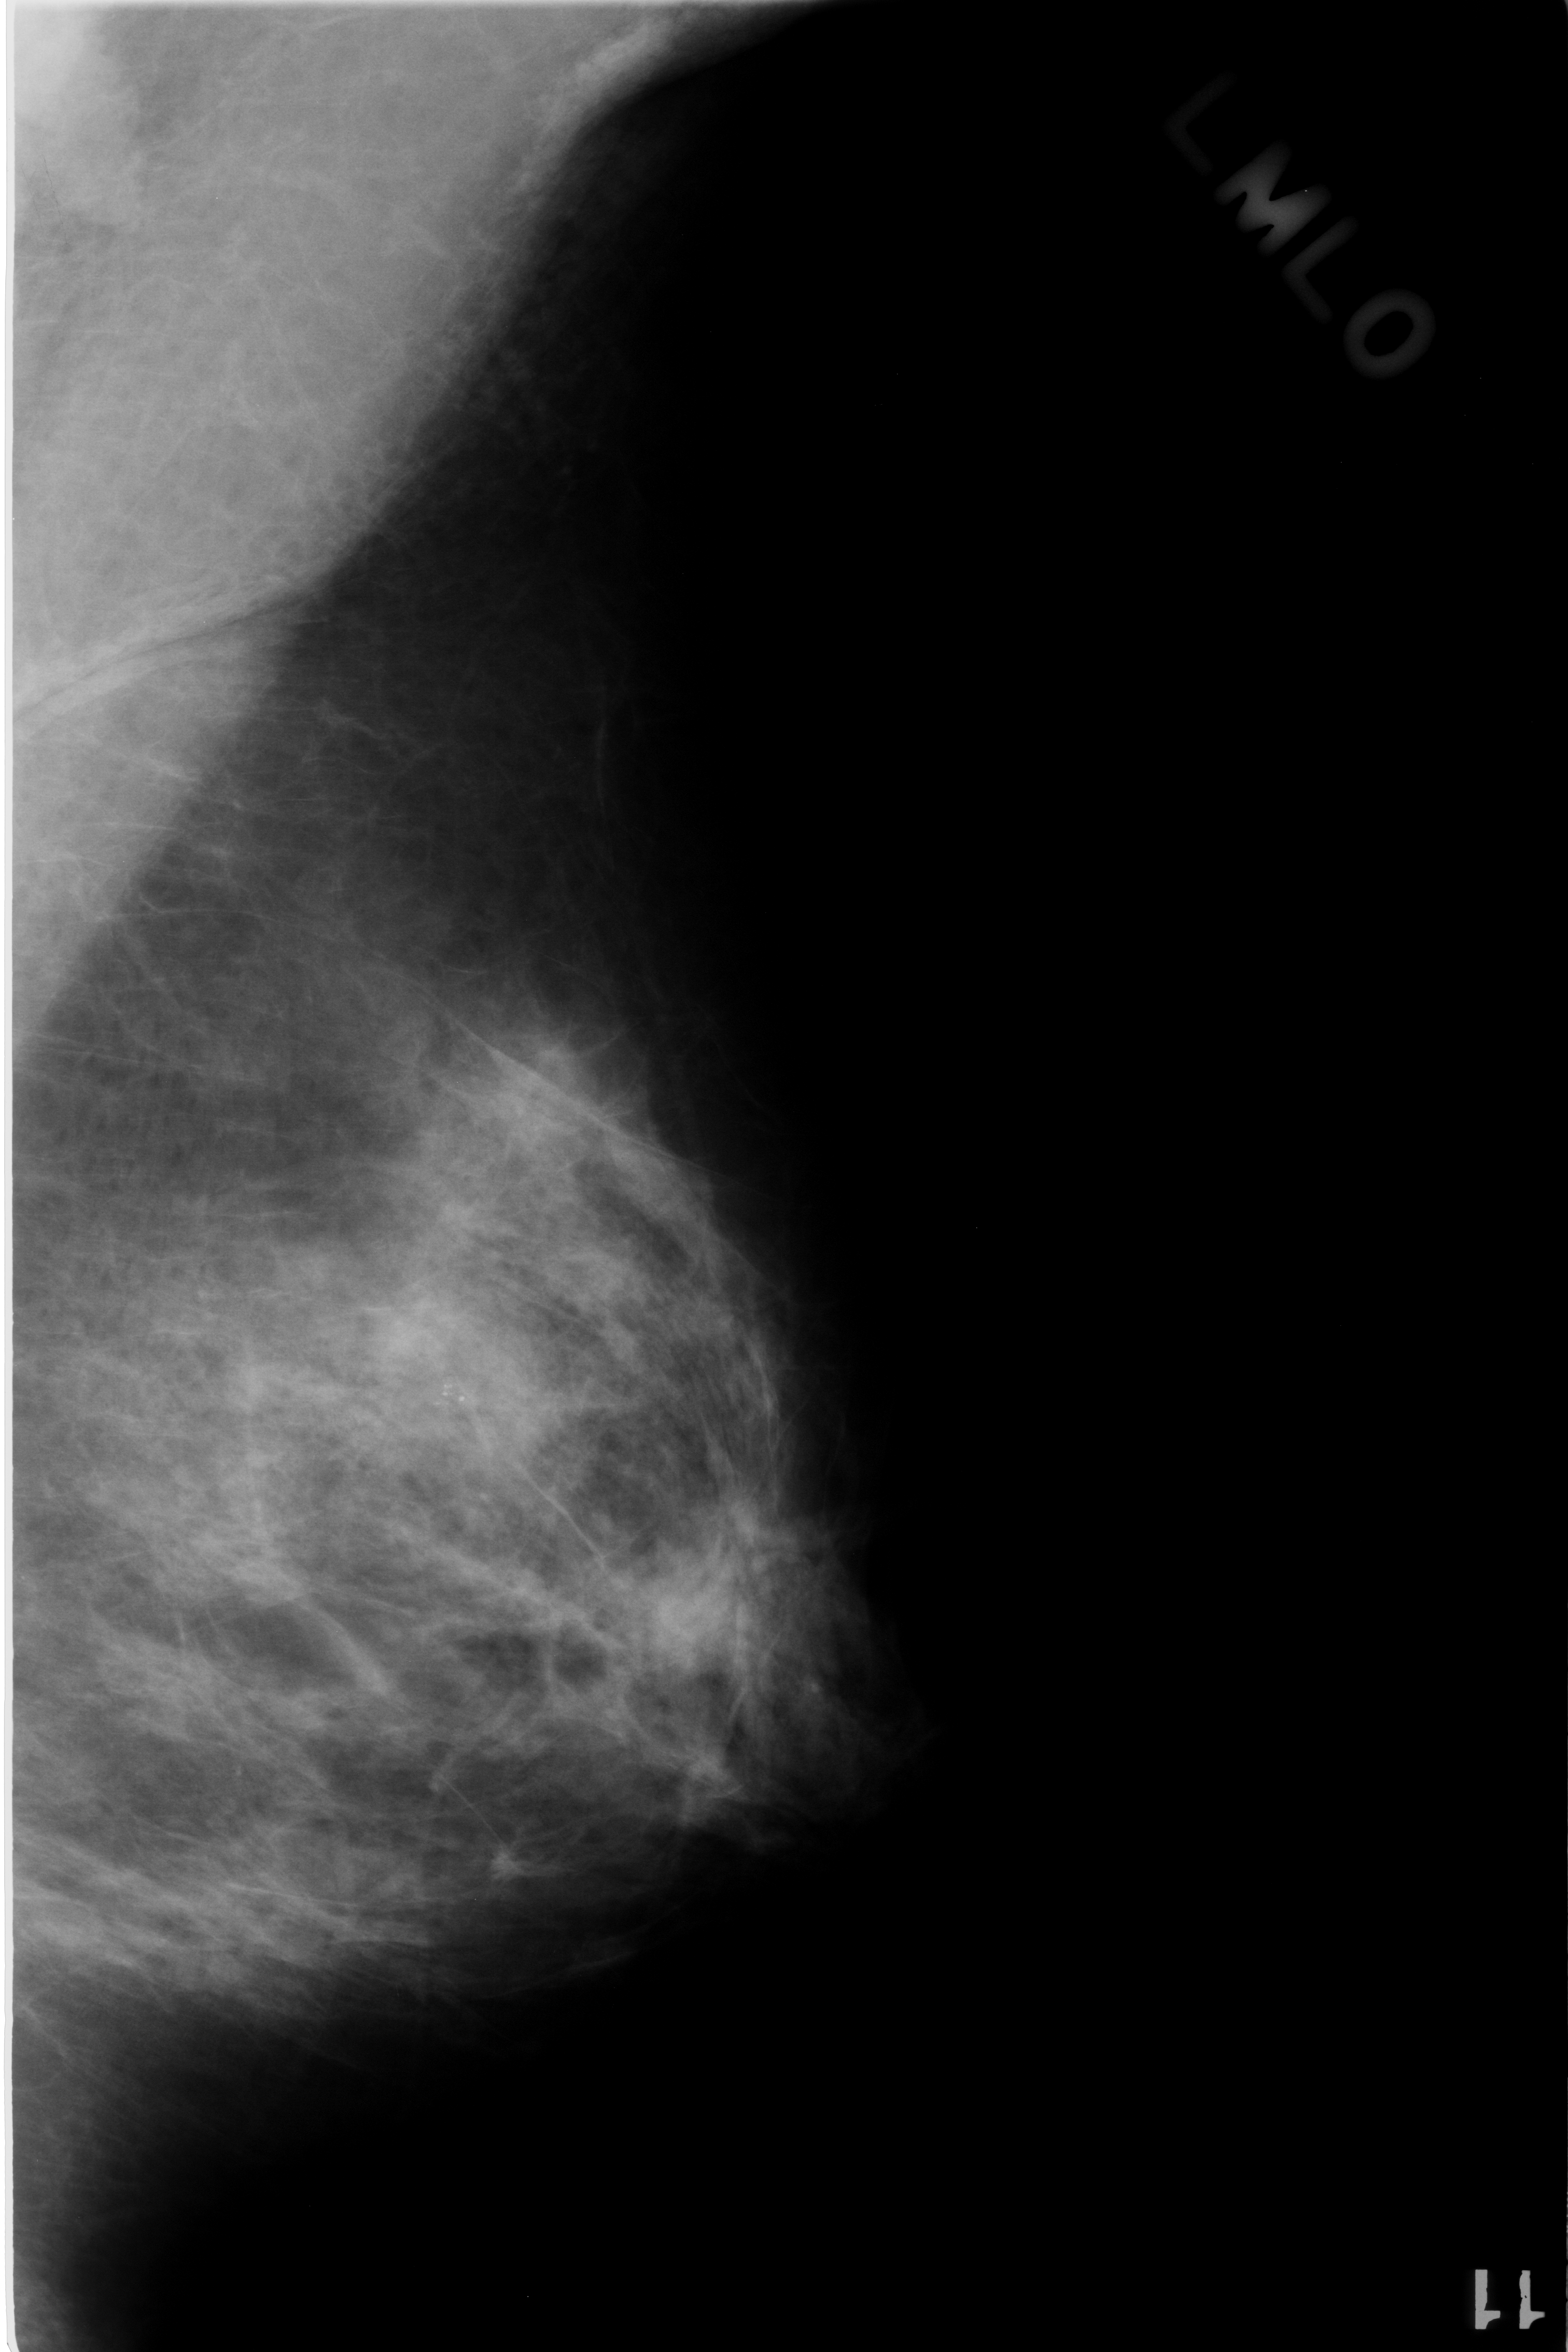
Mammogram (digitized film); left breast; mediolateral oblique (MLO) view; BI-RADS breast density category 2 (scale 1–4); 1568 × 2352 image matrix.
Expert-marked regions of interest on this film, with their recorded descriptors:
- calcifications, morphology punctate, distribution clustered; BI-RADS assessment category 3; subtlety rating 3 on a 1 (subtle) to 5 (obvious) scale; pathology result (as recorded, not read from the image): benign: bounding box <360,1269,553,1449> (left, top, right, bottom; pixels)